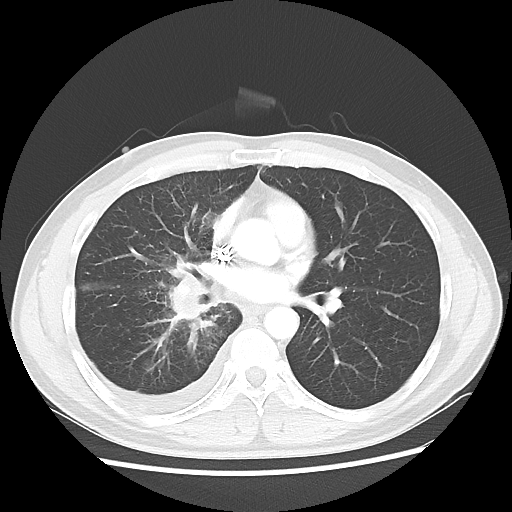
Chest CT, one axial slice. Position 27 of 56 along the scan axis. Reconstruction kernel LUNG. 120 kVp. Lung window (W 1500 / L -600 HU). 512 × 512 image matrix. Patient: male, 46 years. From the clinical record (not read from this slice): clinical TNM (as recorded): T2 N3 M1.
Outlined on this slice (rectangle marked by the reading radiologist):
- lung tumour (recorded histology: adenocarcinoma): bounding box (x1, y1, x2, y2) in pixels: (154, 267, 210, 330)